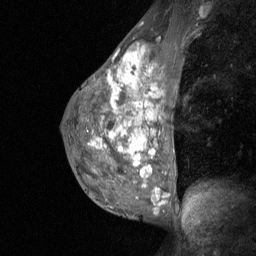
Breast MRI (dynamic contrast-enhanced), one sagittal slice; slice 36 of 64 in the series (ordered by position); dynamic contrast-enhanced study with each time point stored as its own series, time point 2 of 3 at this slice position (early post-contrast, ordered by acquisition time); 1.5 T; TE 4.8 ms, TR 27 ms; 256 × 256 image matrix. Female patient, age 36 years. From the clinical record (not read from this slice): setting: breast cancer imaged before/during neoadjuvant chemotherapy; receptor status: HR-positive, HER2-negative.
Outlined on this slice (semi-automatically segmented with operator editing):
- analysis volume of interest (the breast-tissue region the enhancement analysis was run in; not a lesion): box from (x=73, y=46) to (x=187, y=210) px
- tumour enhancement mask (voxels above the 90 % enhancement threshold inside the analysis volume of interest): (x=119, y=59)–(x=153, y=186)